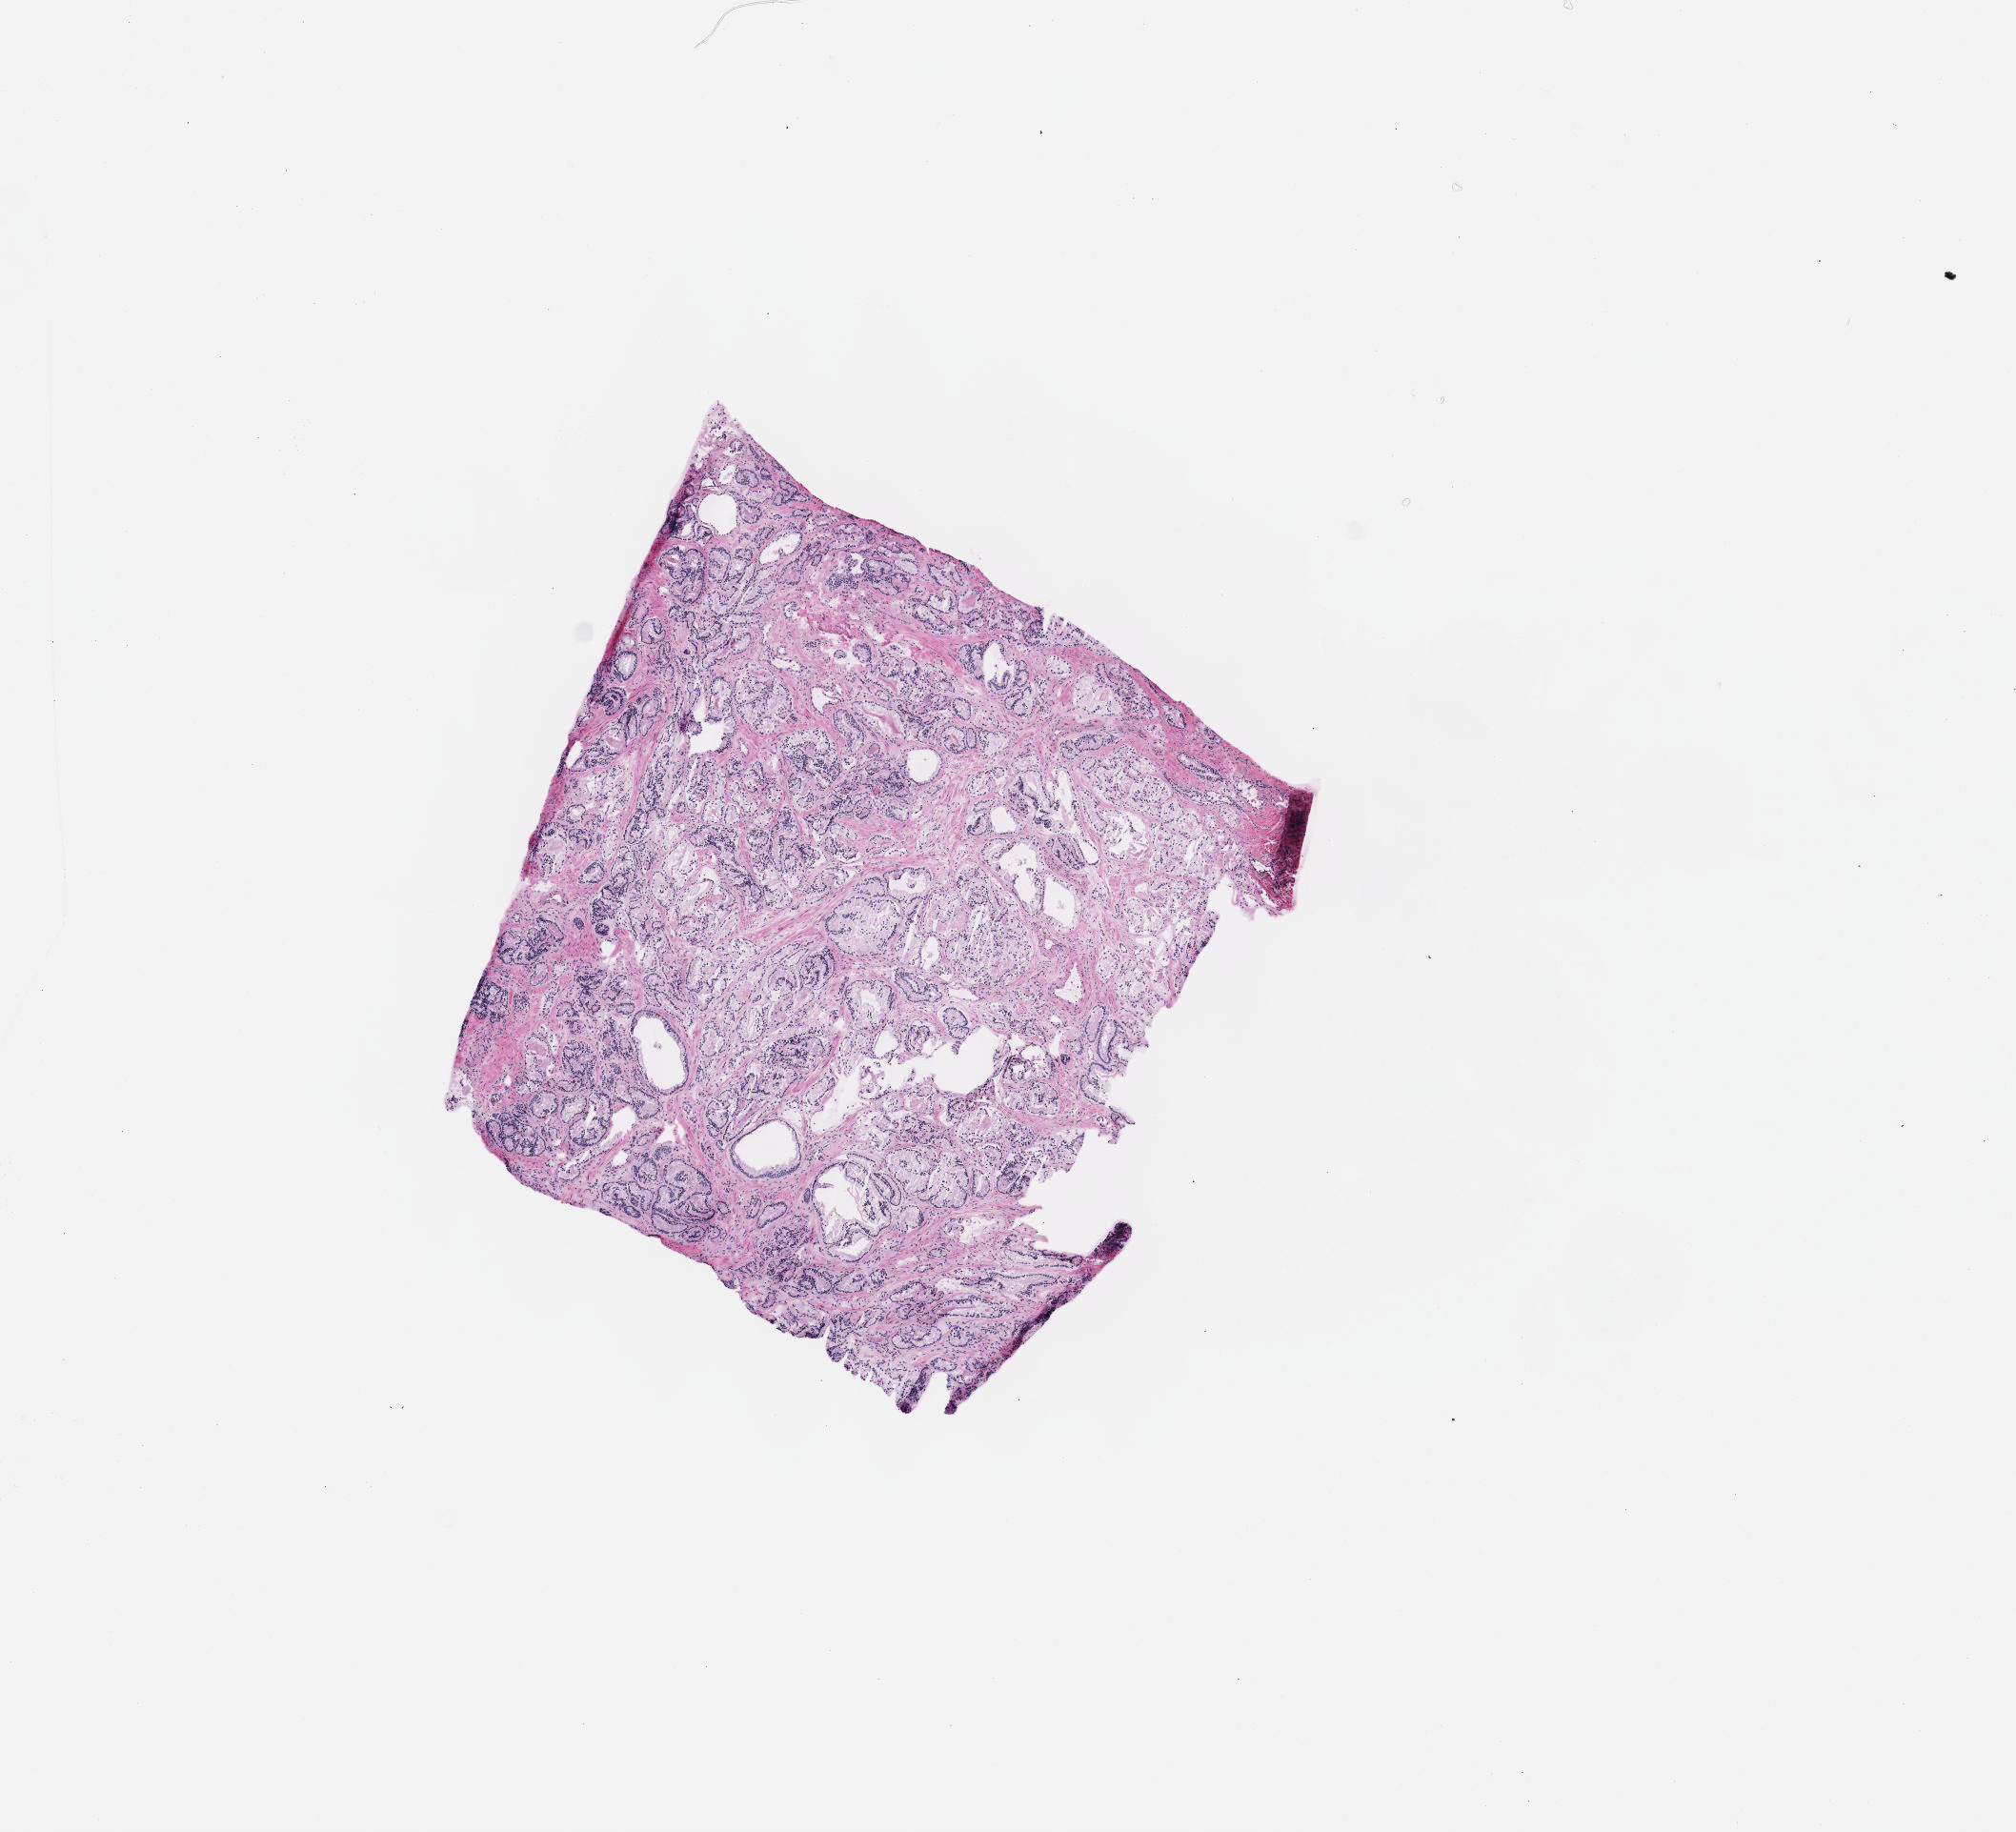
Digitized Hematoxylin and eosin (H&E) stained tissue section (whole slide) — whole scanned area (about 8.6 x 7.8 mm) shown as a low-resolution overview, frozen section from the top of the tissue portion, primary tumour sample from the prostate. Male patient; age at initial diagnosis 67 years. Gleason score: 7 (3+4). Composition of this section per pathologist review: tumour cells 100%, tumour nuclei 60%, normal cells 0%, stromal cells 0%, necrosis 0%. Inflammatory infiltration, as recorded: lymphocyte infiltration 3%, monocyte infiltration 0%, neutrophil infiltration 0%.
- laterality: right
- pathologic diagnosis: Adenocarcinoma, NOS